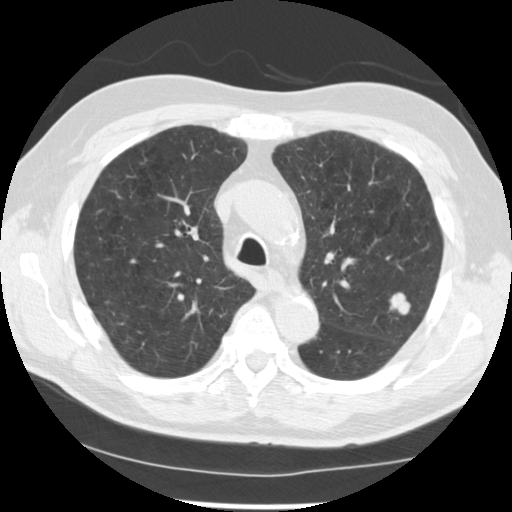
Axial slice from a low-dose chest CT screening exam; first (baseline) screen; lung window (W 1500 / L -600 HU); 2.5 mm slice thickness; slice 173 of 249 in the series; 512 × 512 image matrix. Male participant, aged 71 years at enrolment. Current smoker at enrolment.
• Expert reader's lesion annotation, bounding box (x1, y1, x2, y2) in pixels: (378, 283, 425, 330).
• The screening reader recorded 2 non-calcified nodules or masses ≥4 mm on this exam; which of them this box marks is not recorded.
• Official screen result: positive, change unspecified: nodule(s) >= 4 mm or enlarging nodule(s), mass(es), or other non-specific abnormalities suspicious for lung cancer.